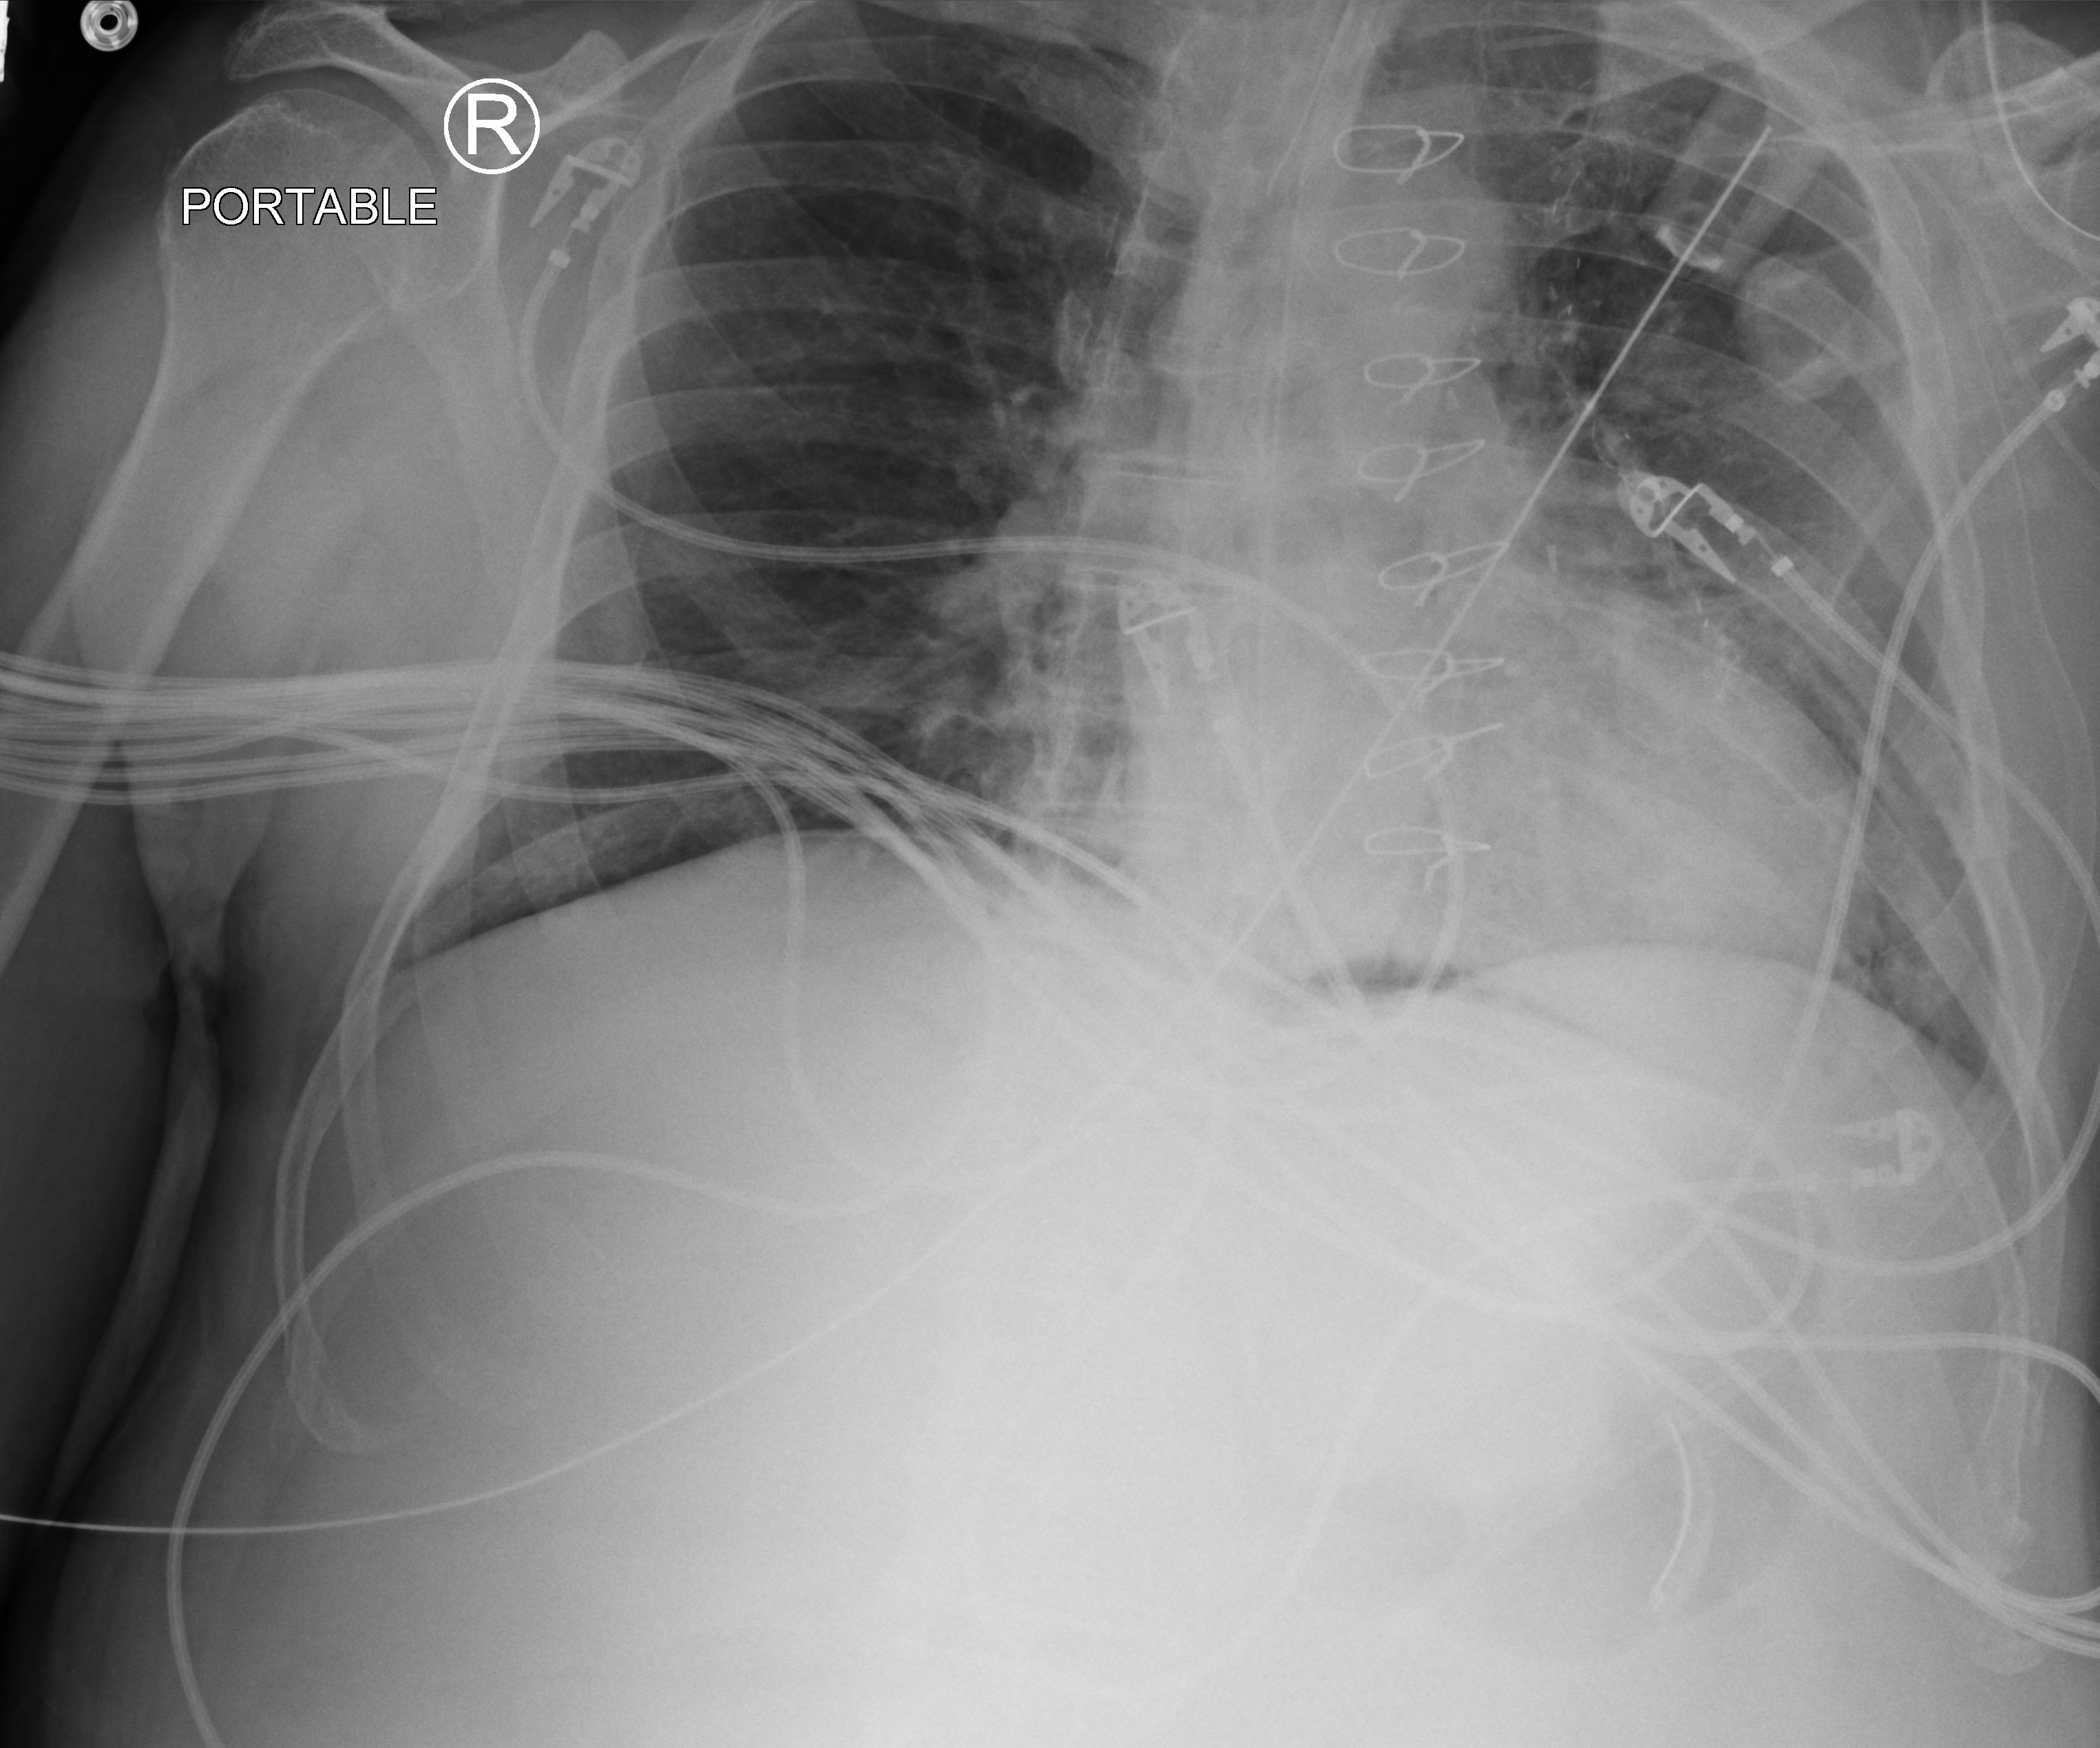
Portable chest radiograph, anteroposterior (AP) projection. Patient hospitalised with COVID-19; male, aged 60–74 years.
Admission-level facts for this patient (not findings on this image; timing relative to this image not recorded): admitted to intensive care during this hospital stay: yes; COPD (admission record): no.